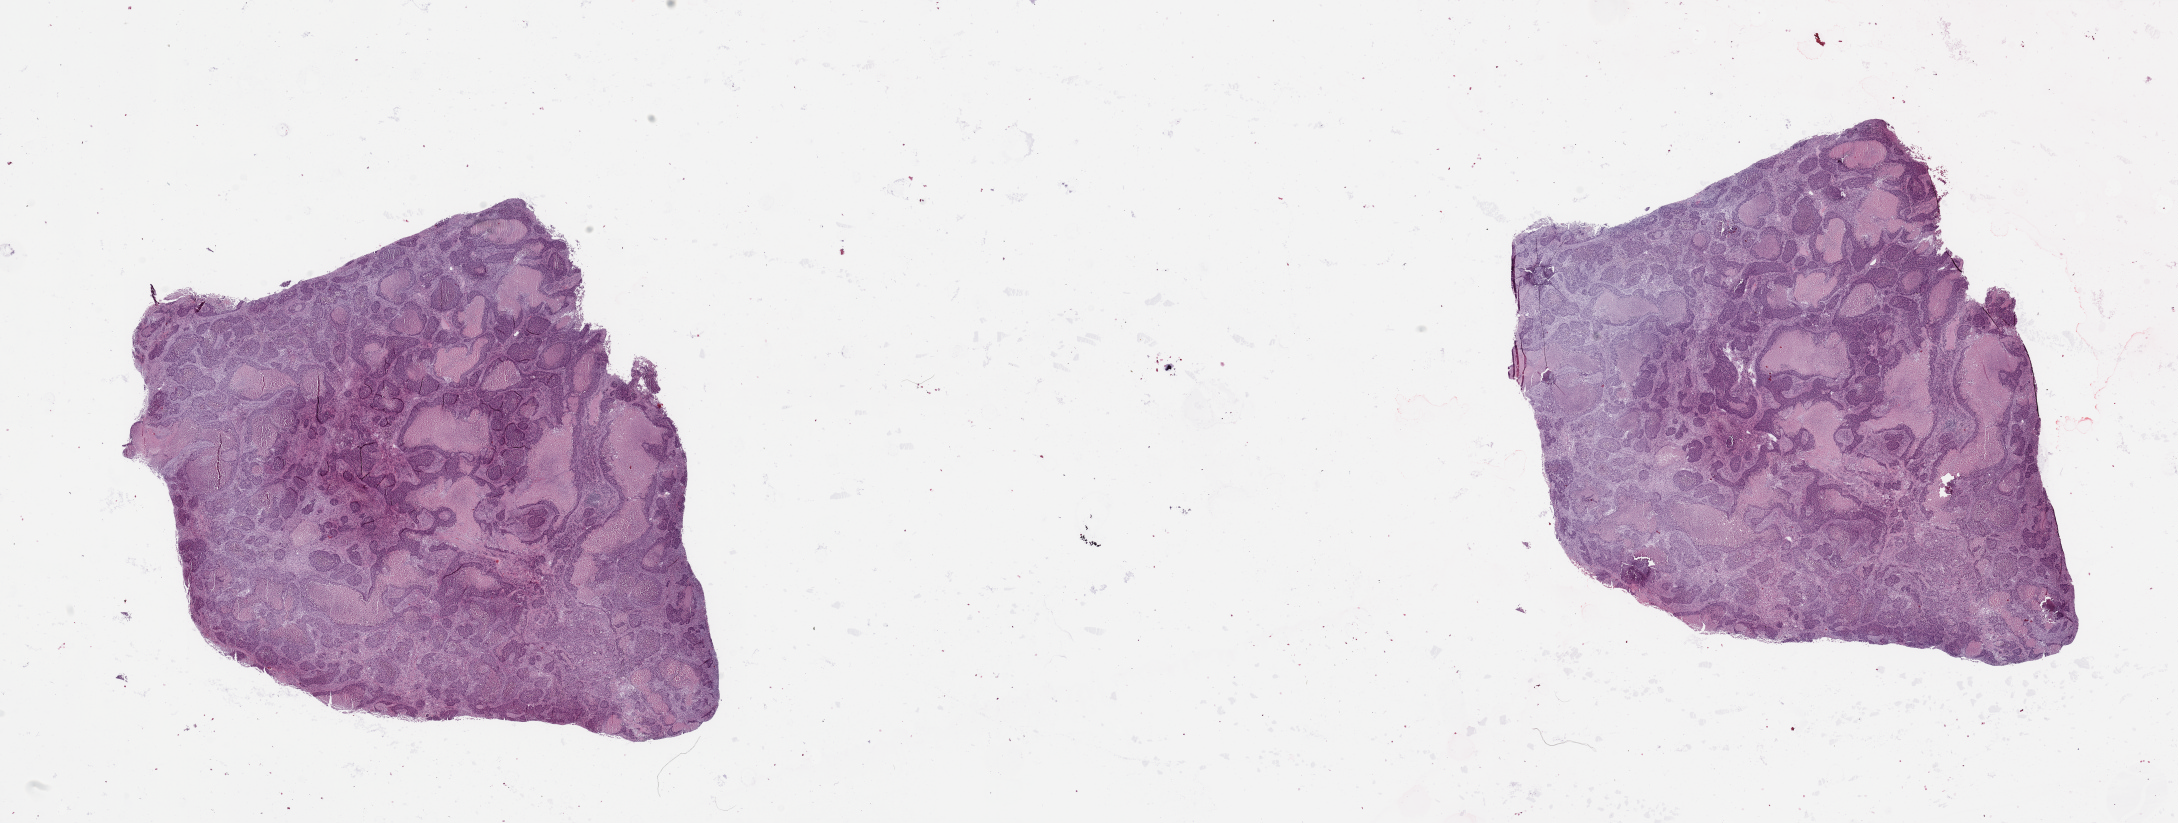
Digitized H&E-stained tissue section (whole slide) — shown as a low-resolution overview of the whole scanned area (about 34.5 x 13.0 mm). Lung, tumour tissue. 62-year-old male patient. Histologic grade: G3 (poorly differentiated).
Histologic diagnosis: Squamous cell carcinoma, NOS. Primary tumour site (as recorded): left lower lobe. AJCC pathologic stage: IIIB.